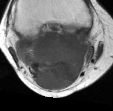
MRI of an extremity soft-tissue mass, one axial slice; position 20 of 45 along the scan axis; MR volume resampled by the dataset authors to the PET/CT grid (not the native acquisition matrix); 3.27 mm slice thickness; 113 × 111 image matrix, field of view 110 × 108 mm. Female patient. From the clinical record (not read from this slice): histological type: liposarcoma; site of the primary tumour: right thigh.
Annotated regions visible in this slice (expert contour drawn on MRI and transferred to this co-registered scan by the dataset authors):
- gross tumour volume (mass): box from (x=22, y=30) to (x=93, y=91) px